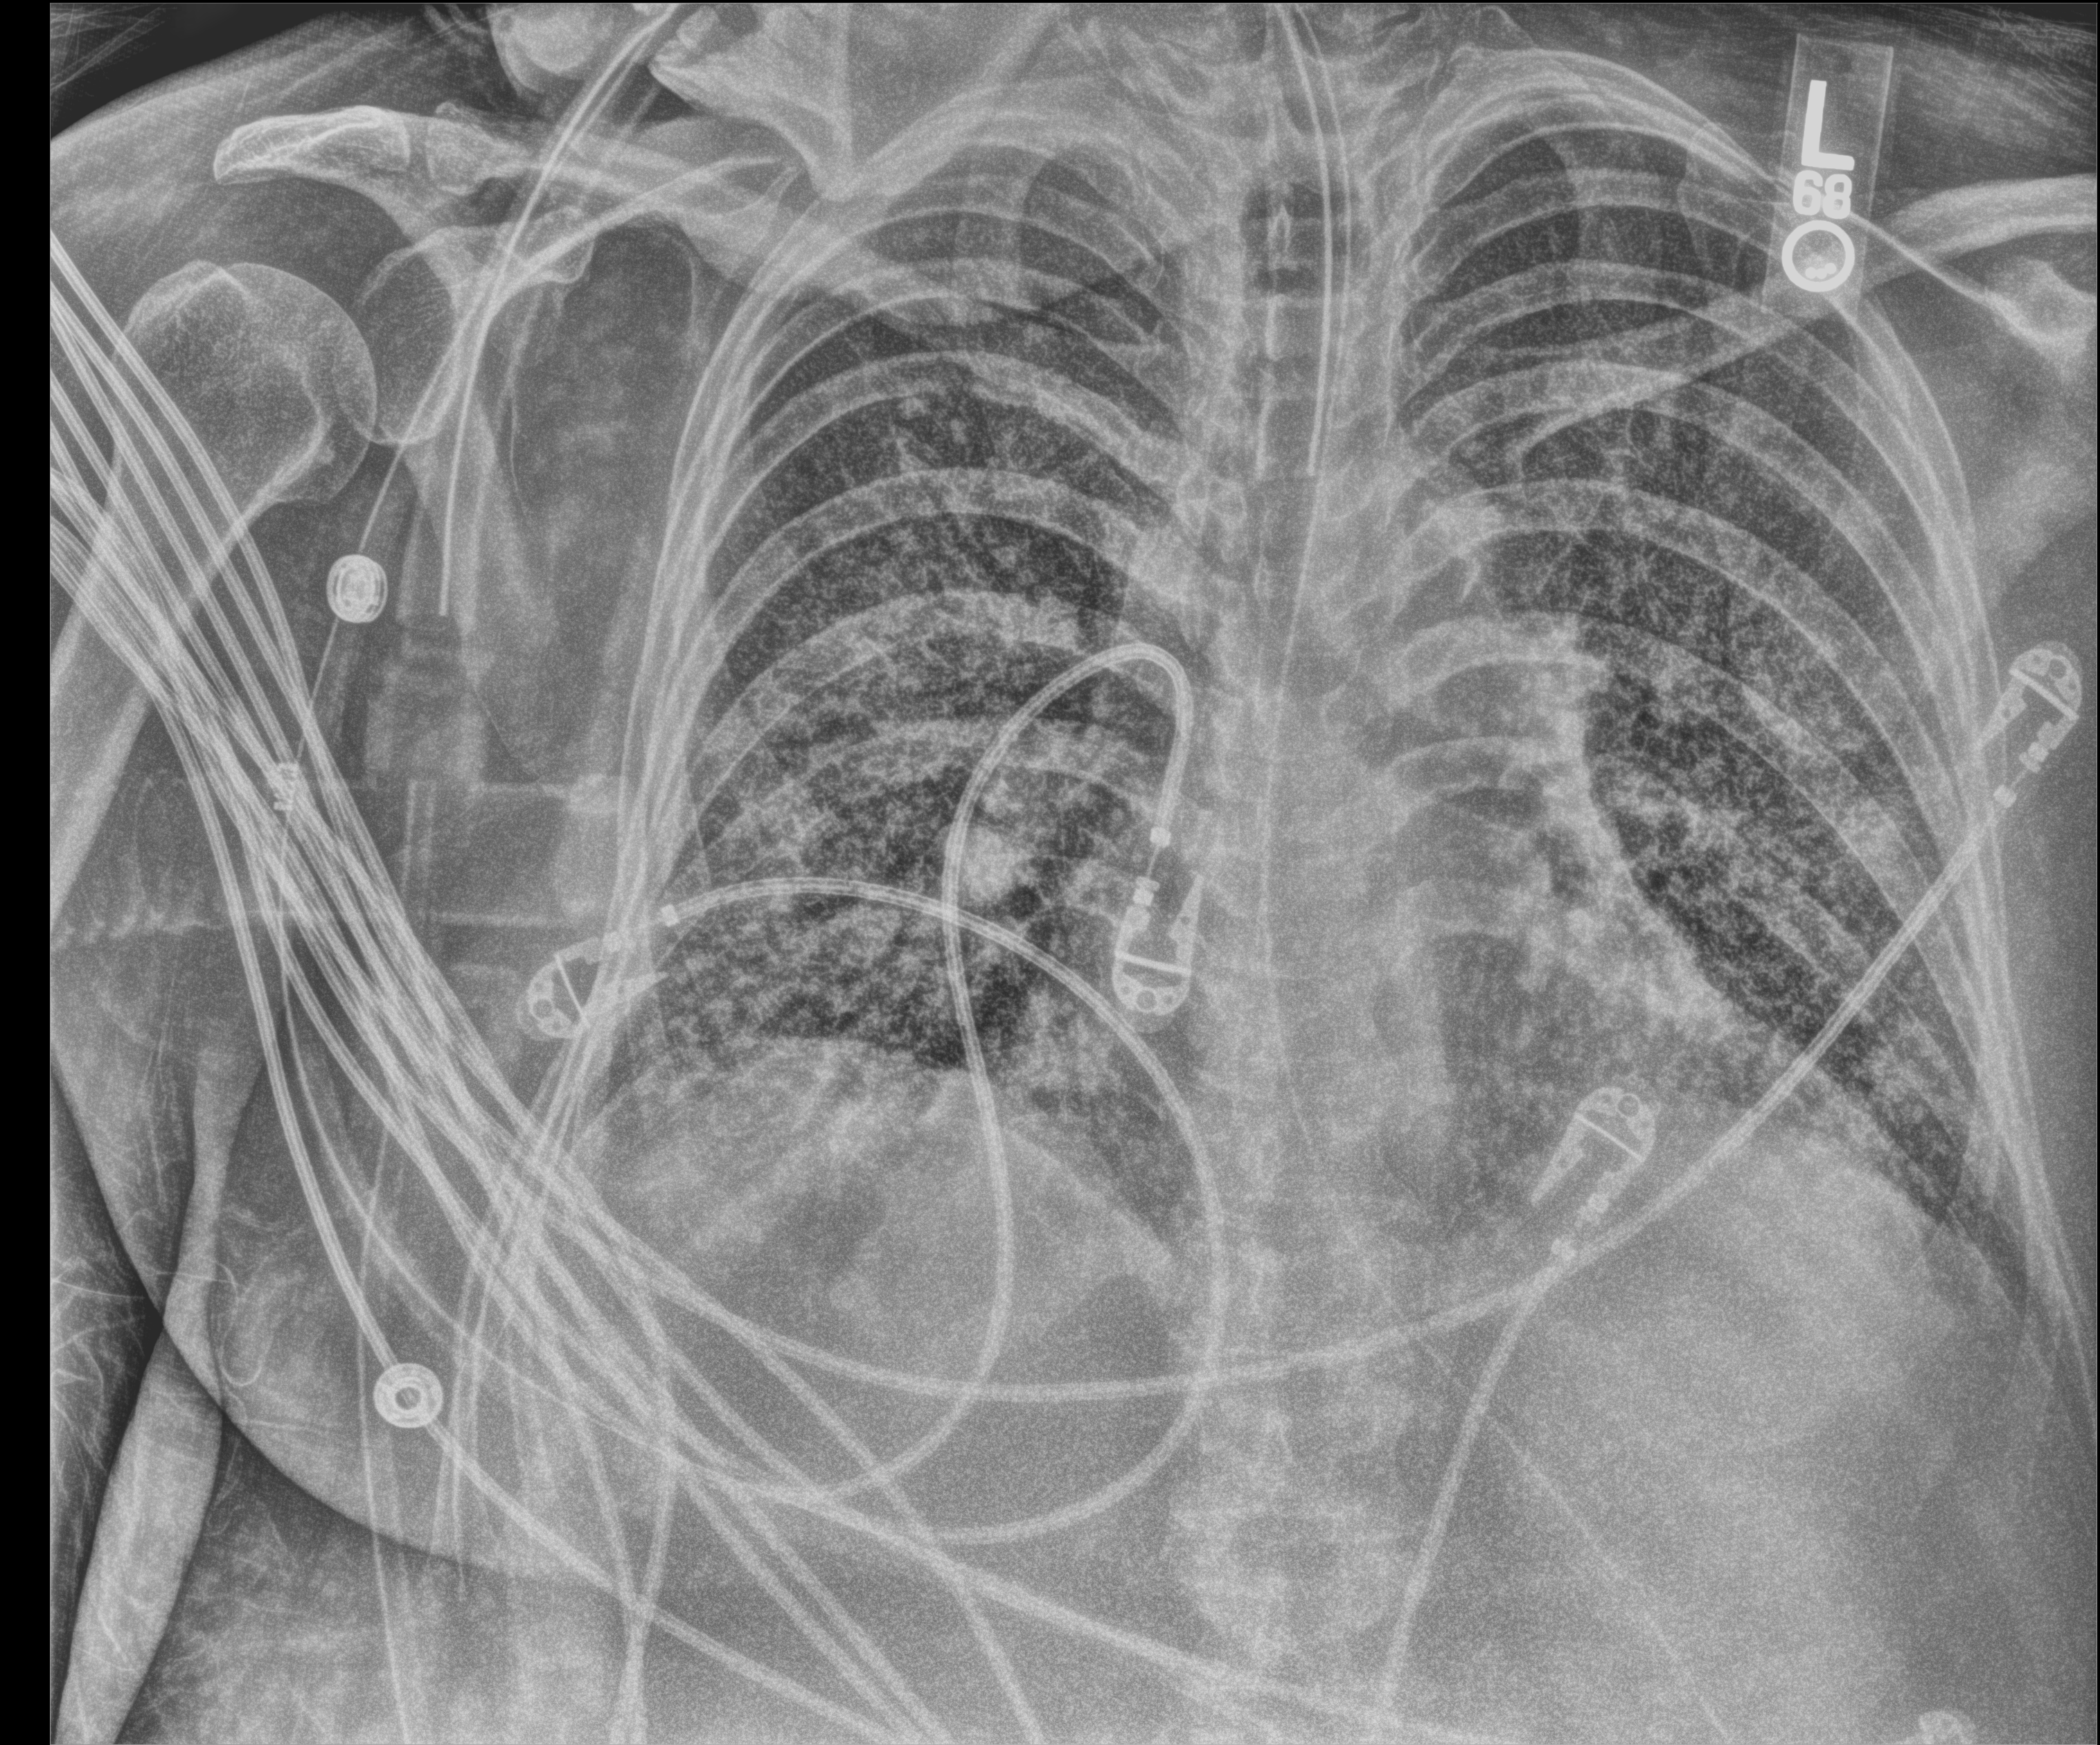
Chest X-ray (portable); anteroposterior (AP) projection. Adult patient hospitalised with COVID-19, age 18–59 years.
From the hospital-stay record, not from the radiograph (when in the stay this image was taken is not recorded):
- diabetes (admission record): no